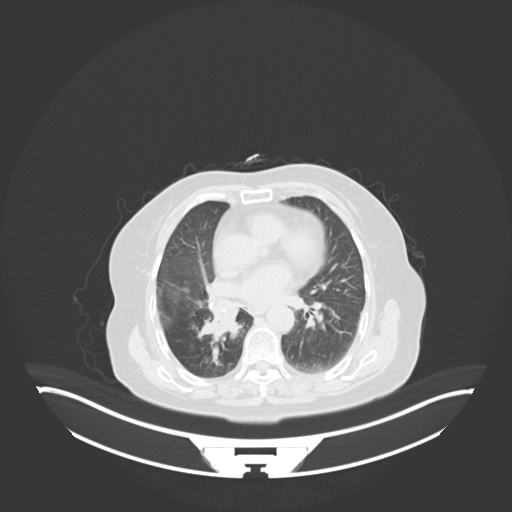
Chest CT, one axial slice; position 26 of 76 along the scan axis; 120 kVp; lung window (W 1500 / L -600 HU); 3 mm slice thickness; 512 × 512 image matrix, field of view 500 × 500 mm. Patient: female, 75 years. Case-level facts recorded for this patient, not image findings: clinical TNM (as recorded): T1b N0 M1a.
Structures marked on this image (rectangle marked by the reading radiologist):
- lung tumour (recorded histology: squamous cell carcinoma): bounding box <198,293,241,347> (left, top, right, bottom; pixels)